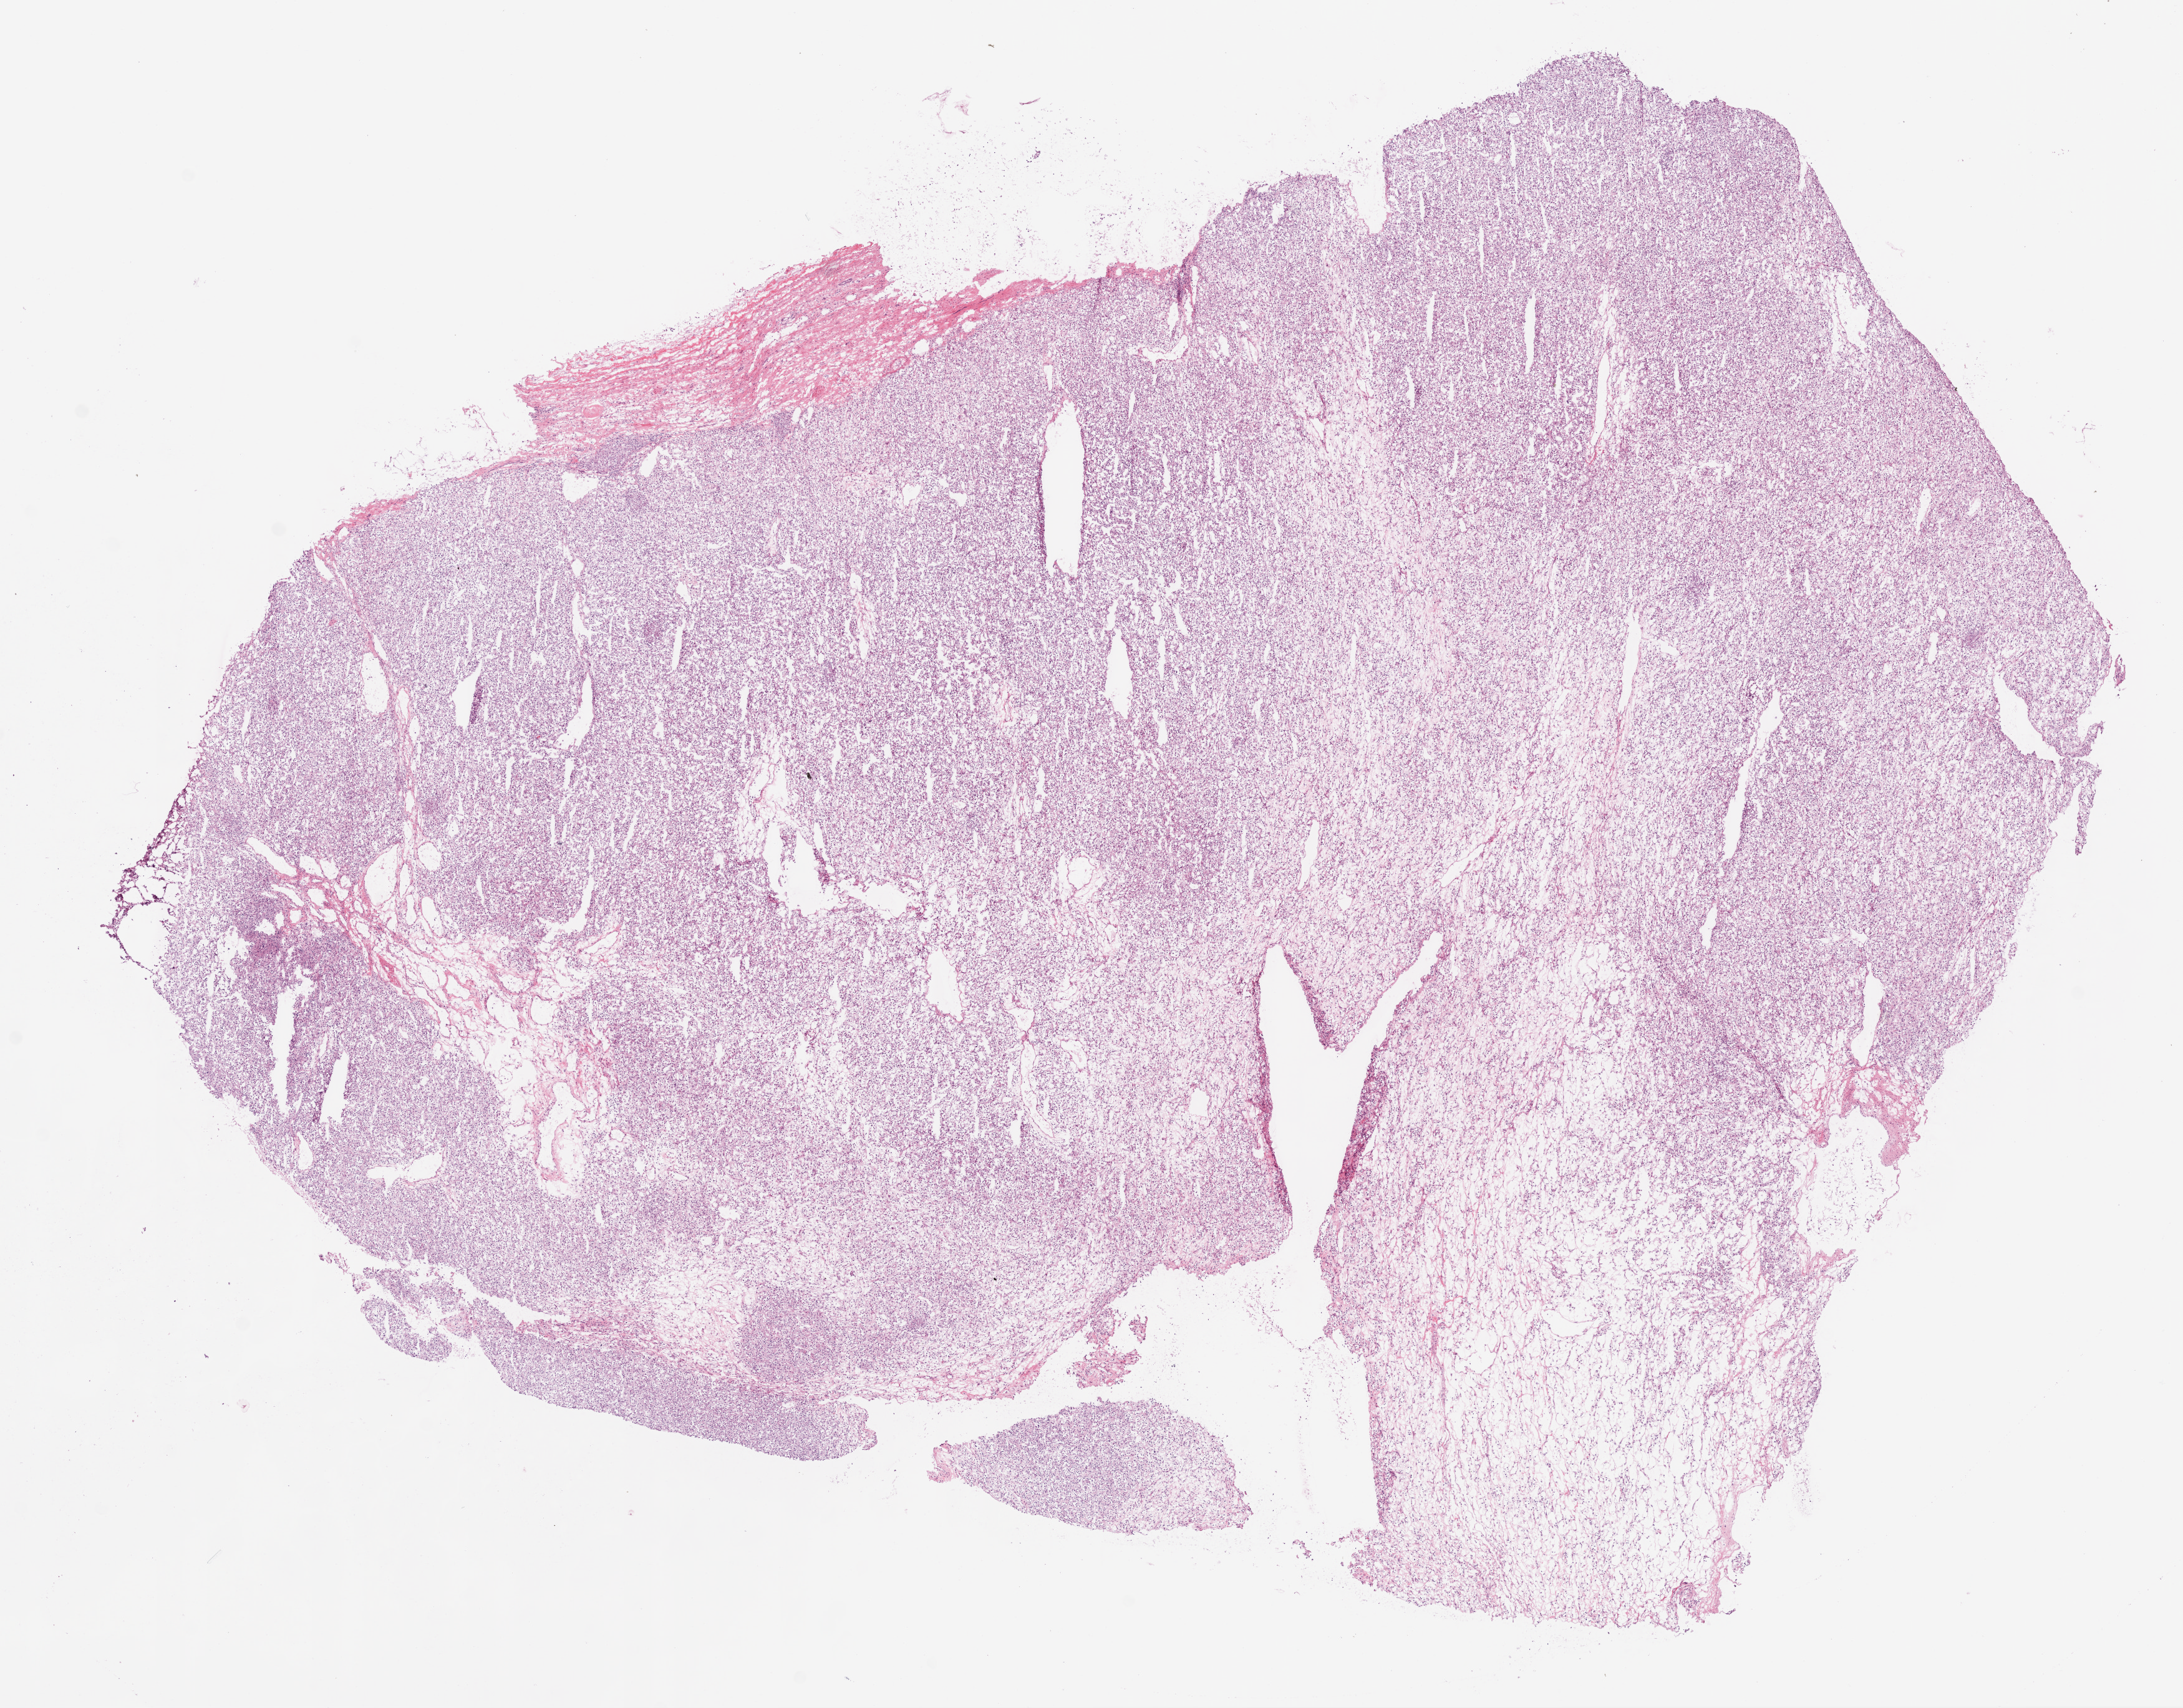
Digitized Hematoxylin and eosin (H&E) stained tissue section (whole slide) — shown as a low-resolution overview of the whole scanned area (about 14.0 x 11.0 mm, acquisition: 20x scan), frozen section from the bottom of the tissue portion, primary tumour sample from the kidney. Male patient; age at initial diagnosis 43 years. Histologic grade: G3 (poorly differentiated). Composition of this section per pathologist review: tumour cells 90%, tumour nuclei 85%, normal cells 0%, stromal cells 10%, necrosis 0%.
- AJCC pathologic stage: IV
- pathologic diagnosis: Clear cell adenocarcinoma, NOS
- TNM: T2 N0 M1